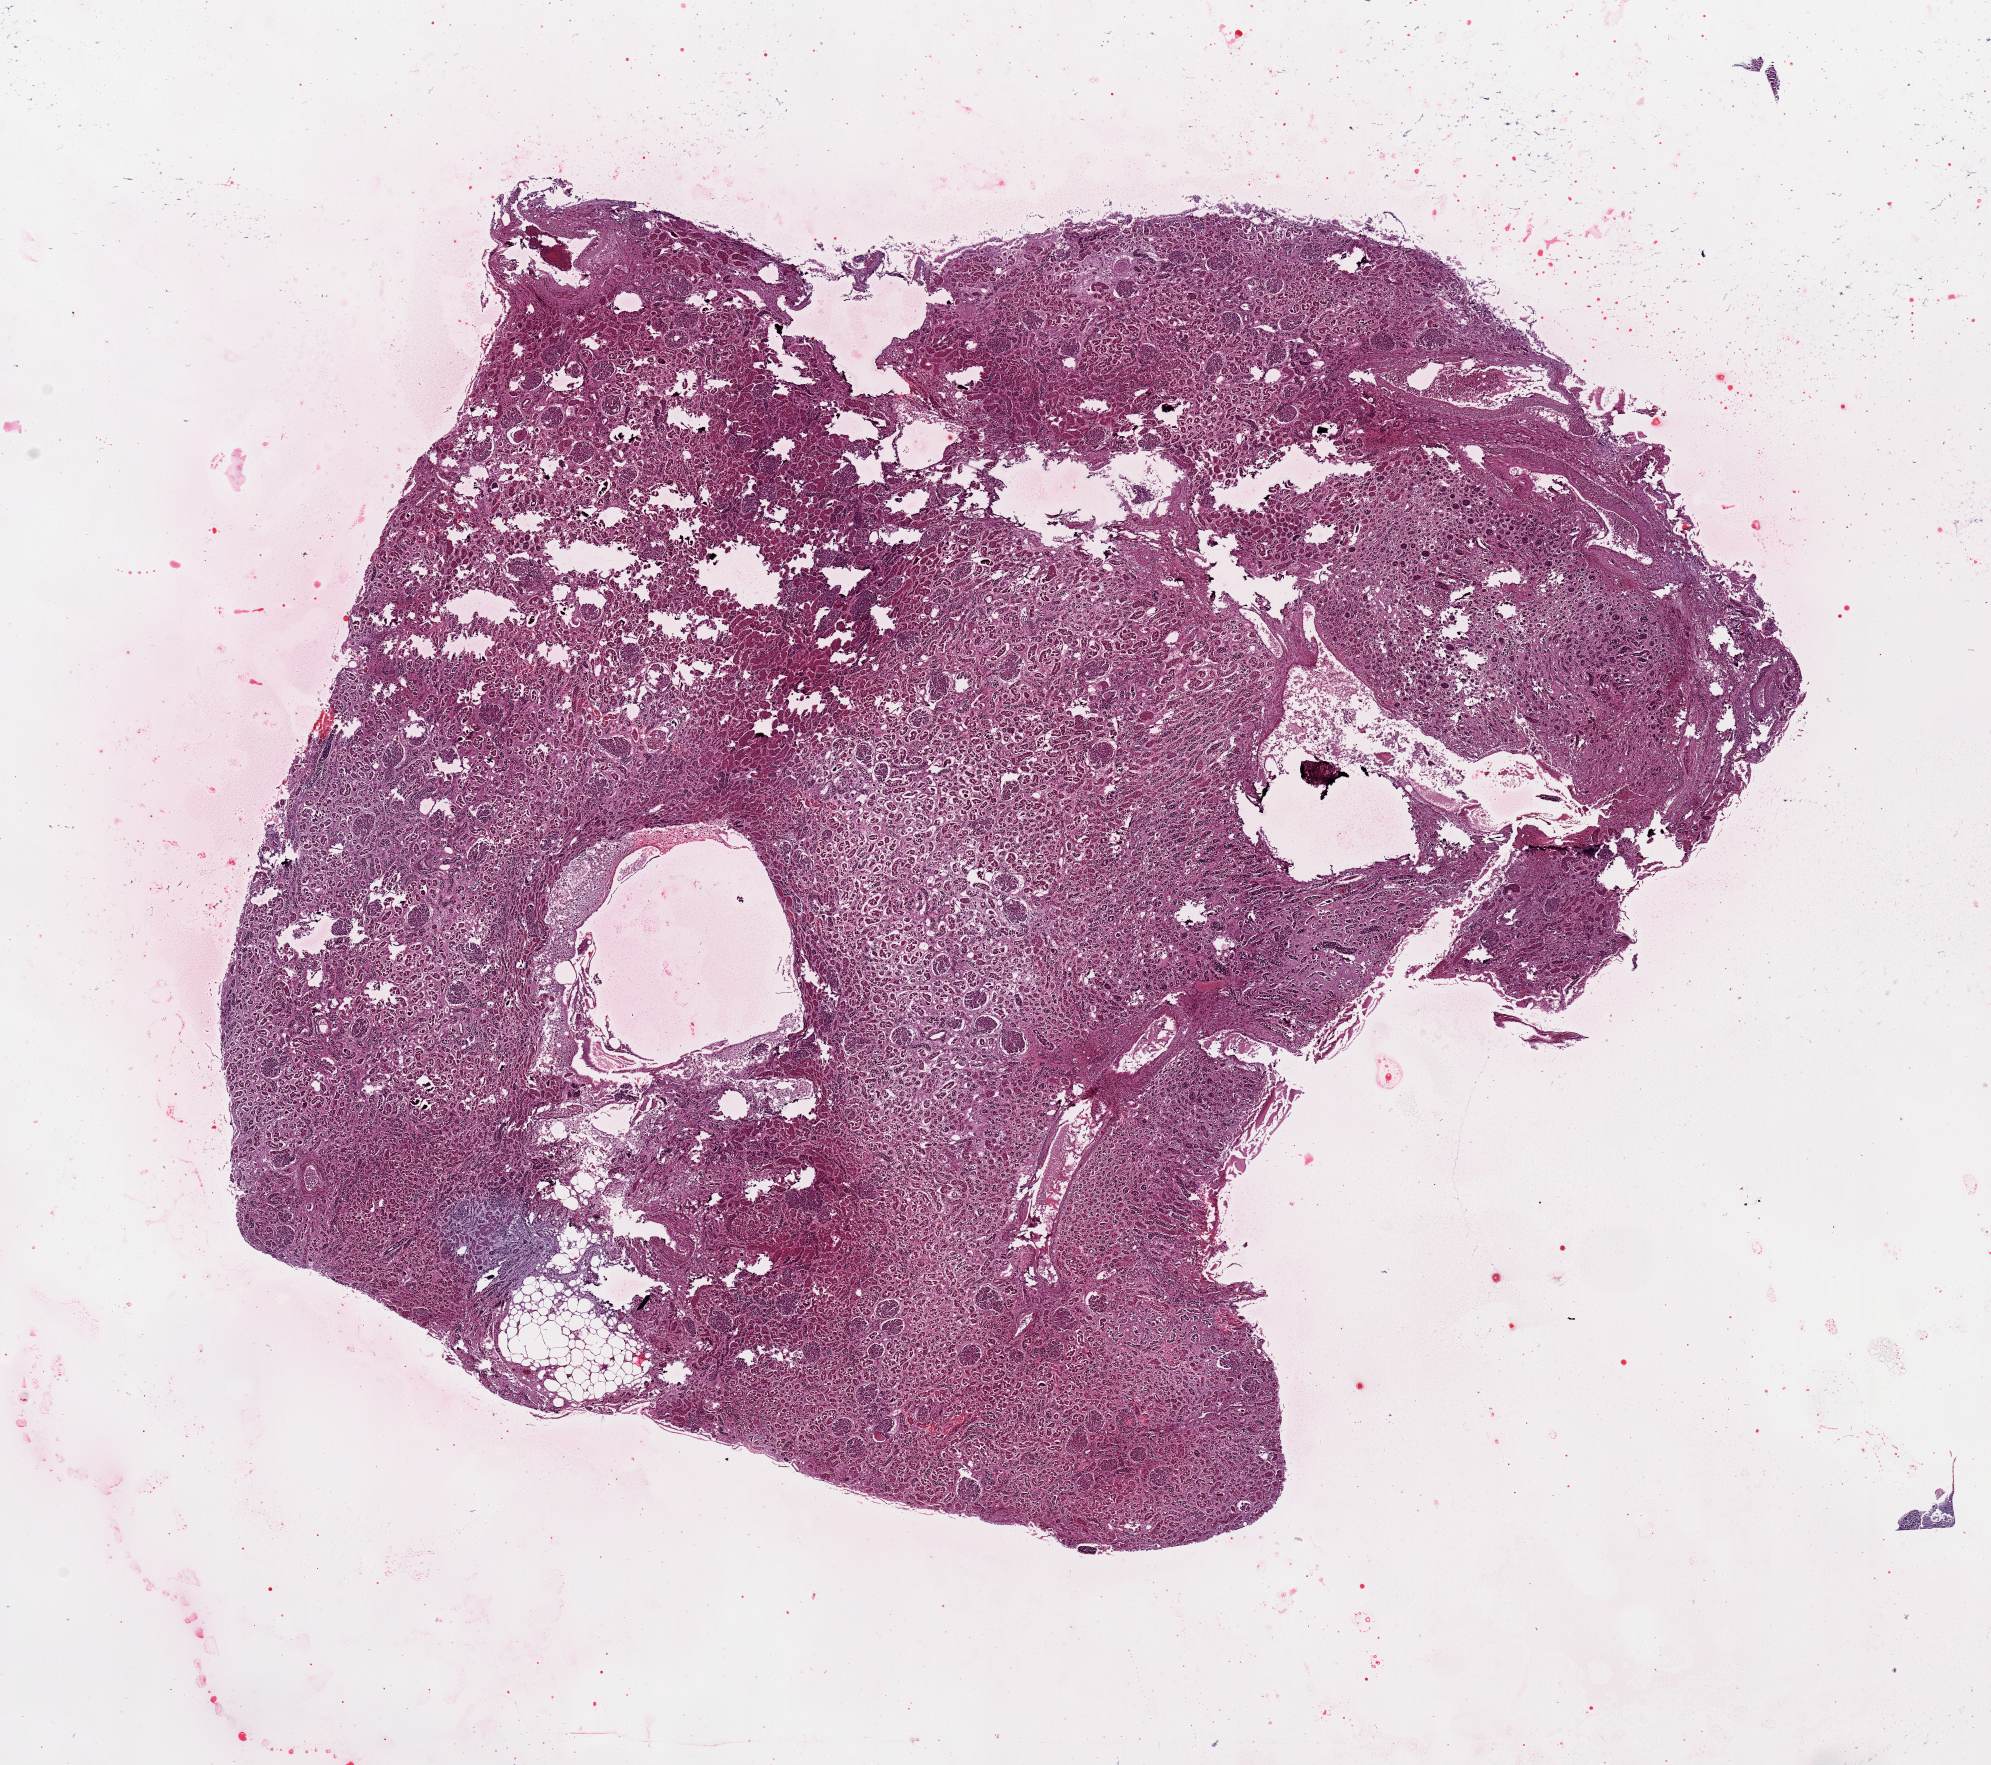
Haematoxylin and eosin whole-slide image — whole scanned area (about 15.8 x 14.0 mm, acquisition: 20x scan) shown as a low-resolution overview. PAXgene-fixed paraffin-embedded (PFPE) section. Sampled site (target tissue): renal medulla. Tissue donor sample. Female donor.
Pathologist's review note for this sample: Mostly cortex. Severe fractures.